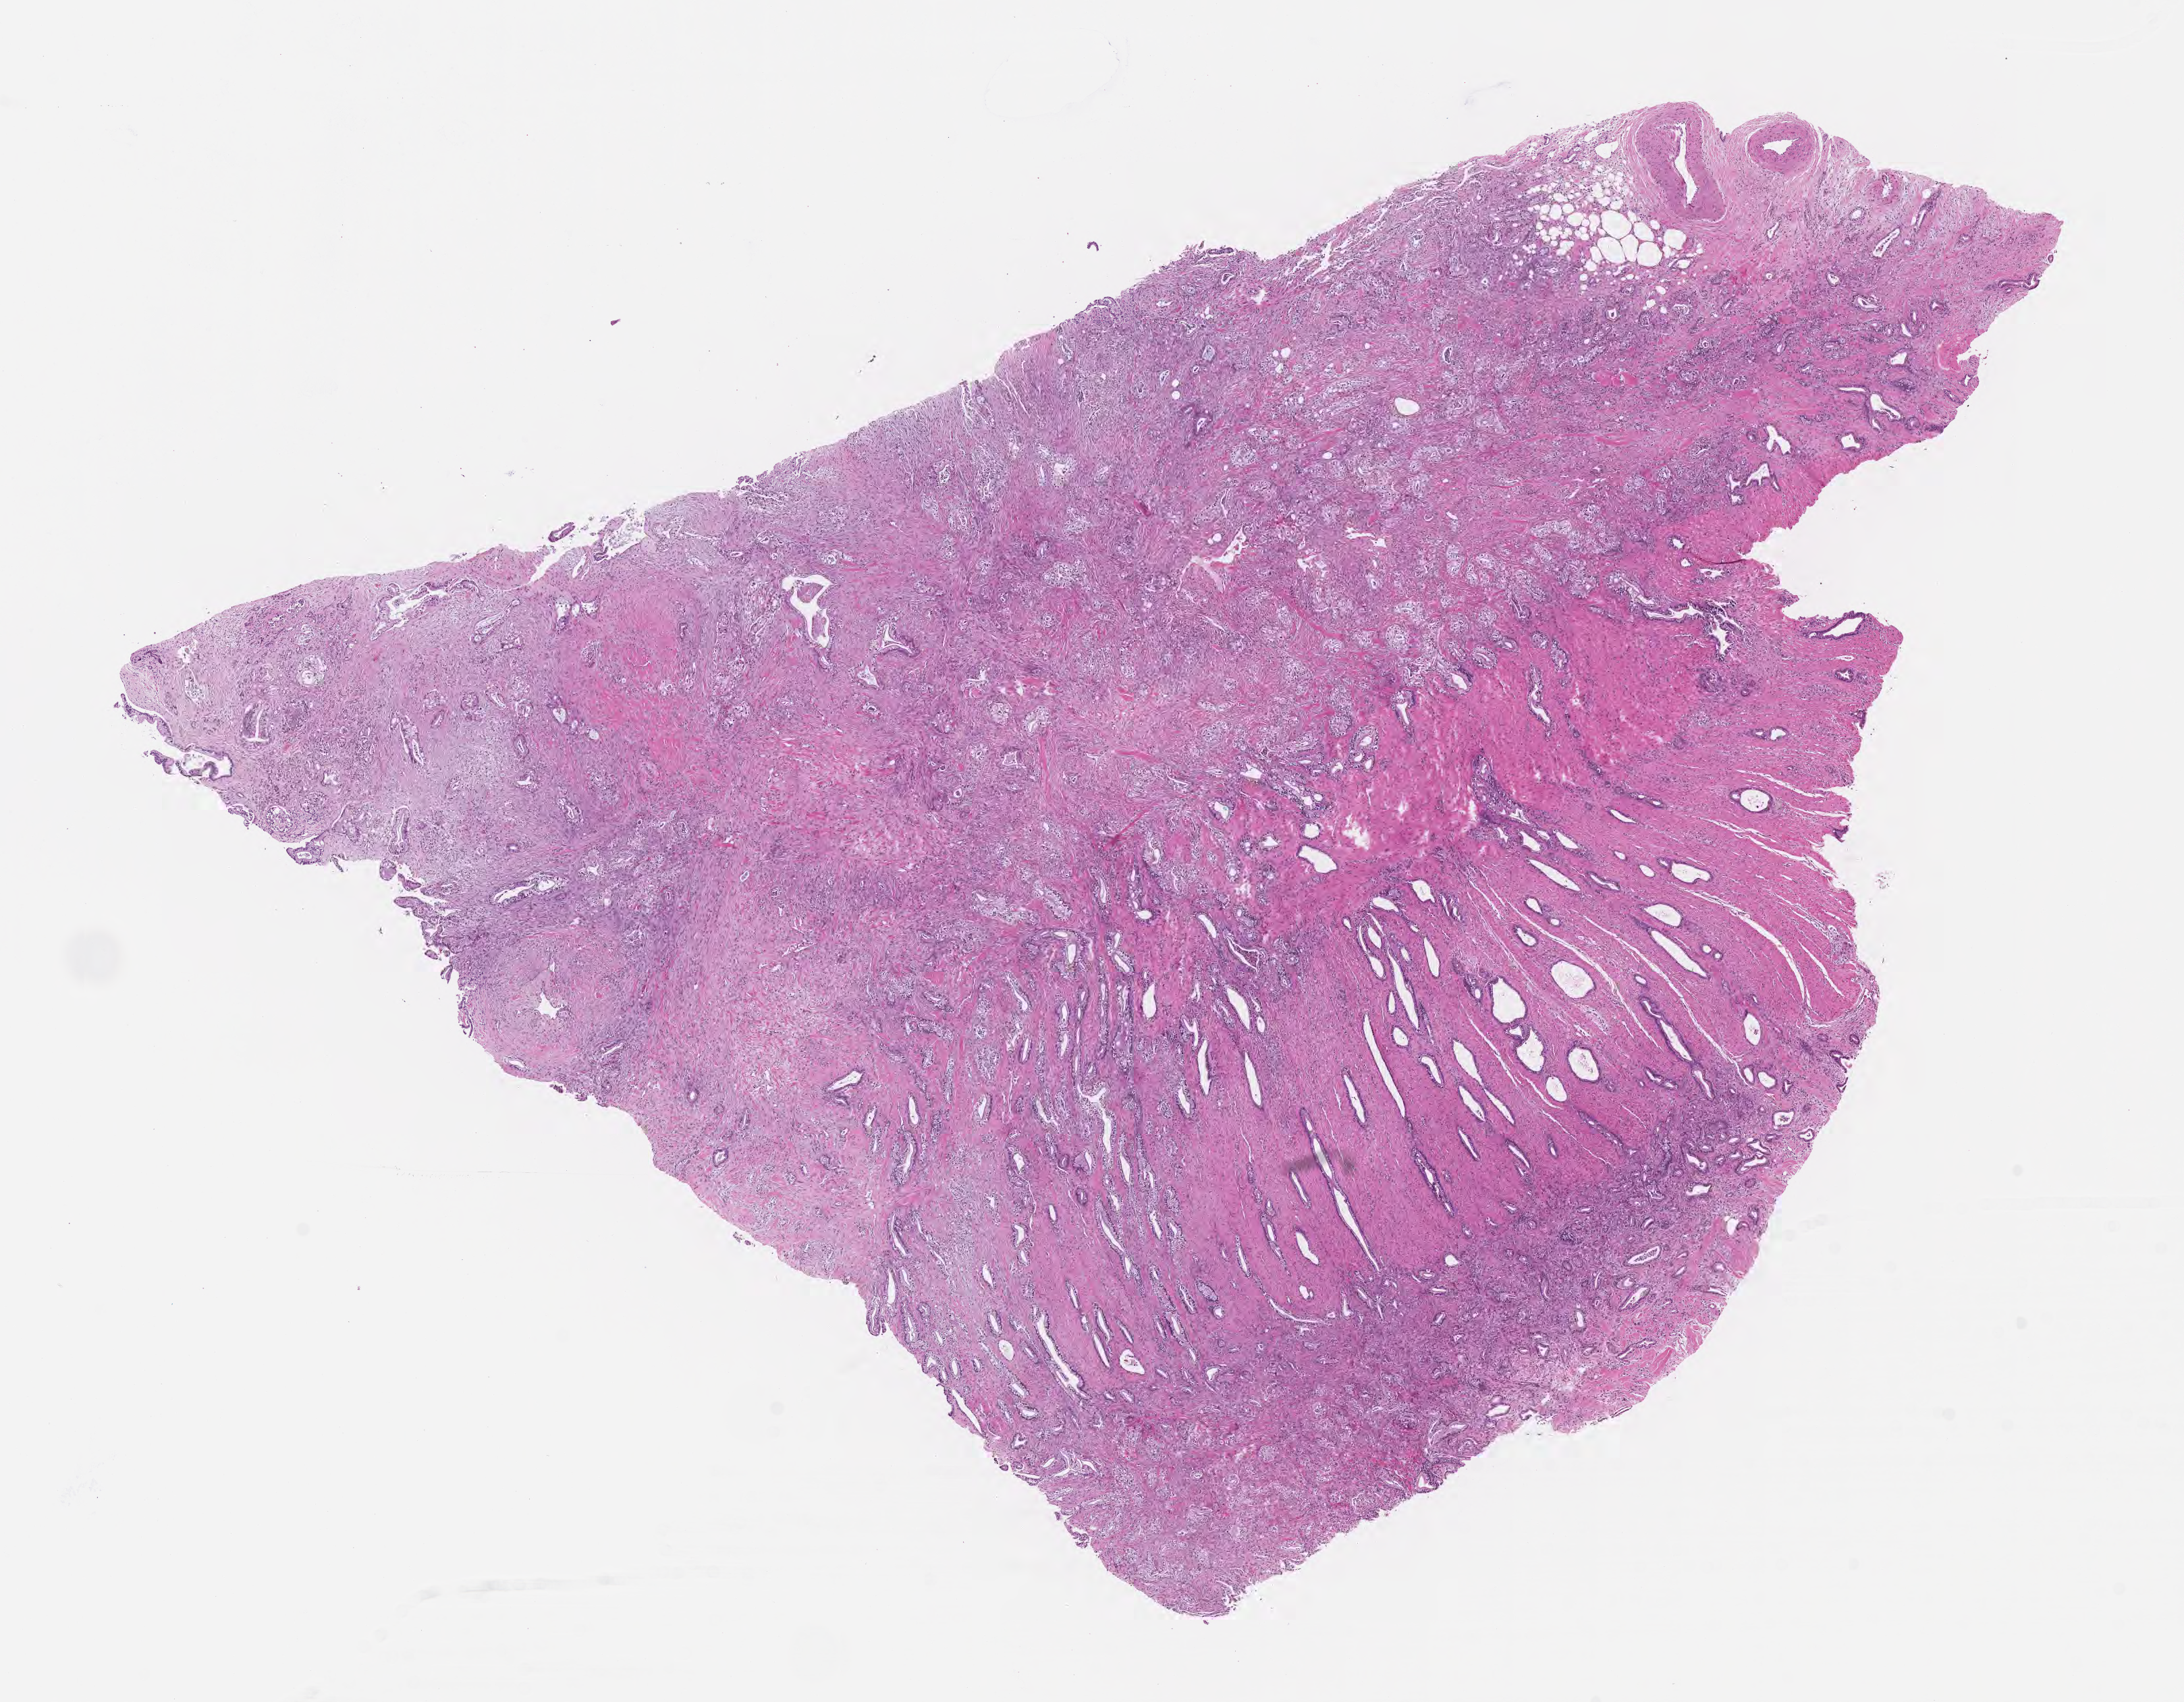
Whole-slide image, haematoxylin and eosin stain, a low-resolution overview of the entire scanned area, about 13.1 x 10.2 mm; FFPE section; primary tumor; site: head of pancreas. Patient: male, age at initial diagnosis 63 years. Tumor grade: G2 (moderately differentiated). Slide review estimates, as recorded: tumor cells 50%, tumor nuclei 60%, stromal cells 25%, necrosis 0%, normal cells 25%. Infiltration values recorded for this section: lymphocyte infiltration 0%, monocyte infiltration 0%, neutrophil infiltration 0%.
• AJCC pathologic stage: Stage IB
• histologic diagnosis: Infiltrating duct carcinoma, NOS